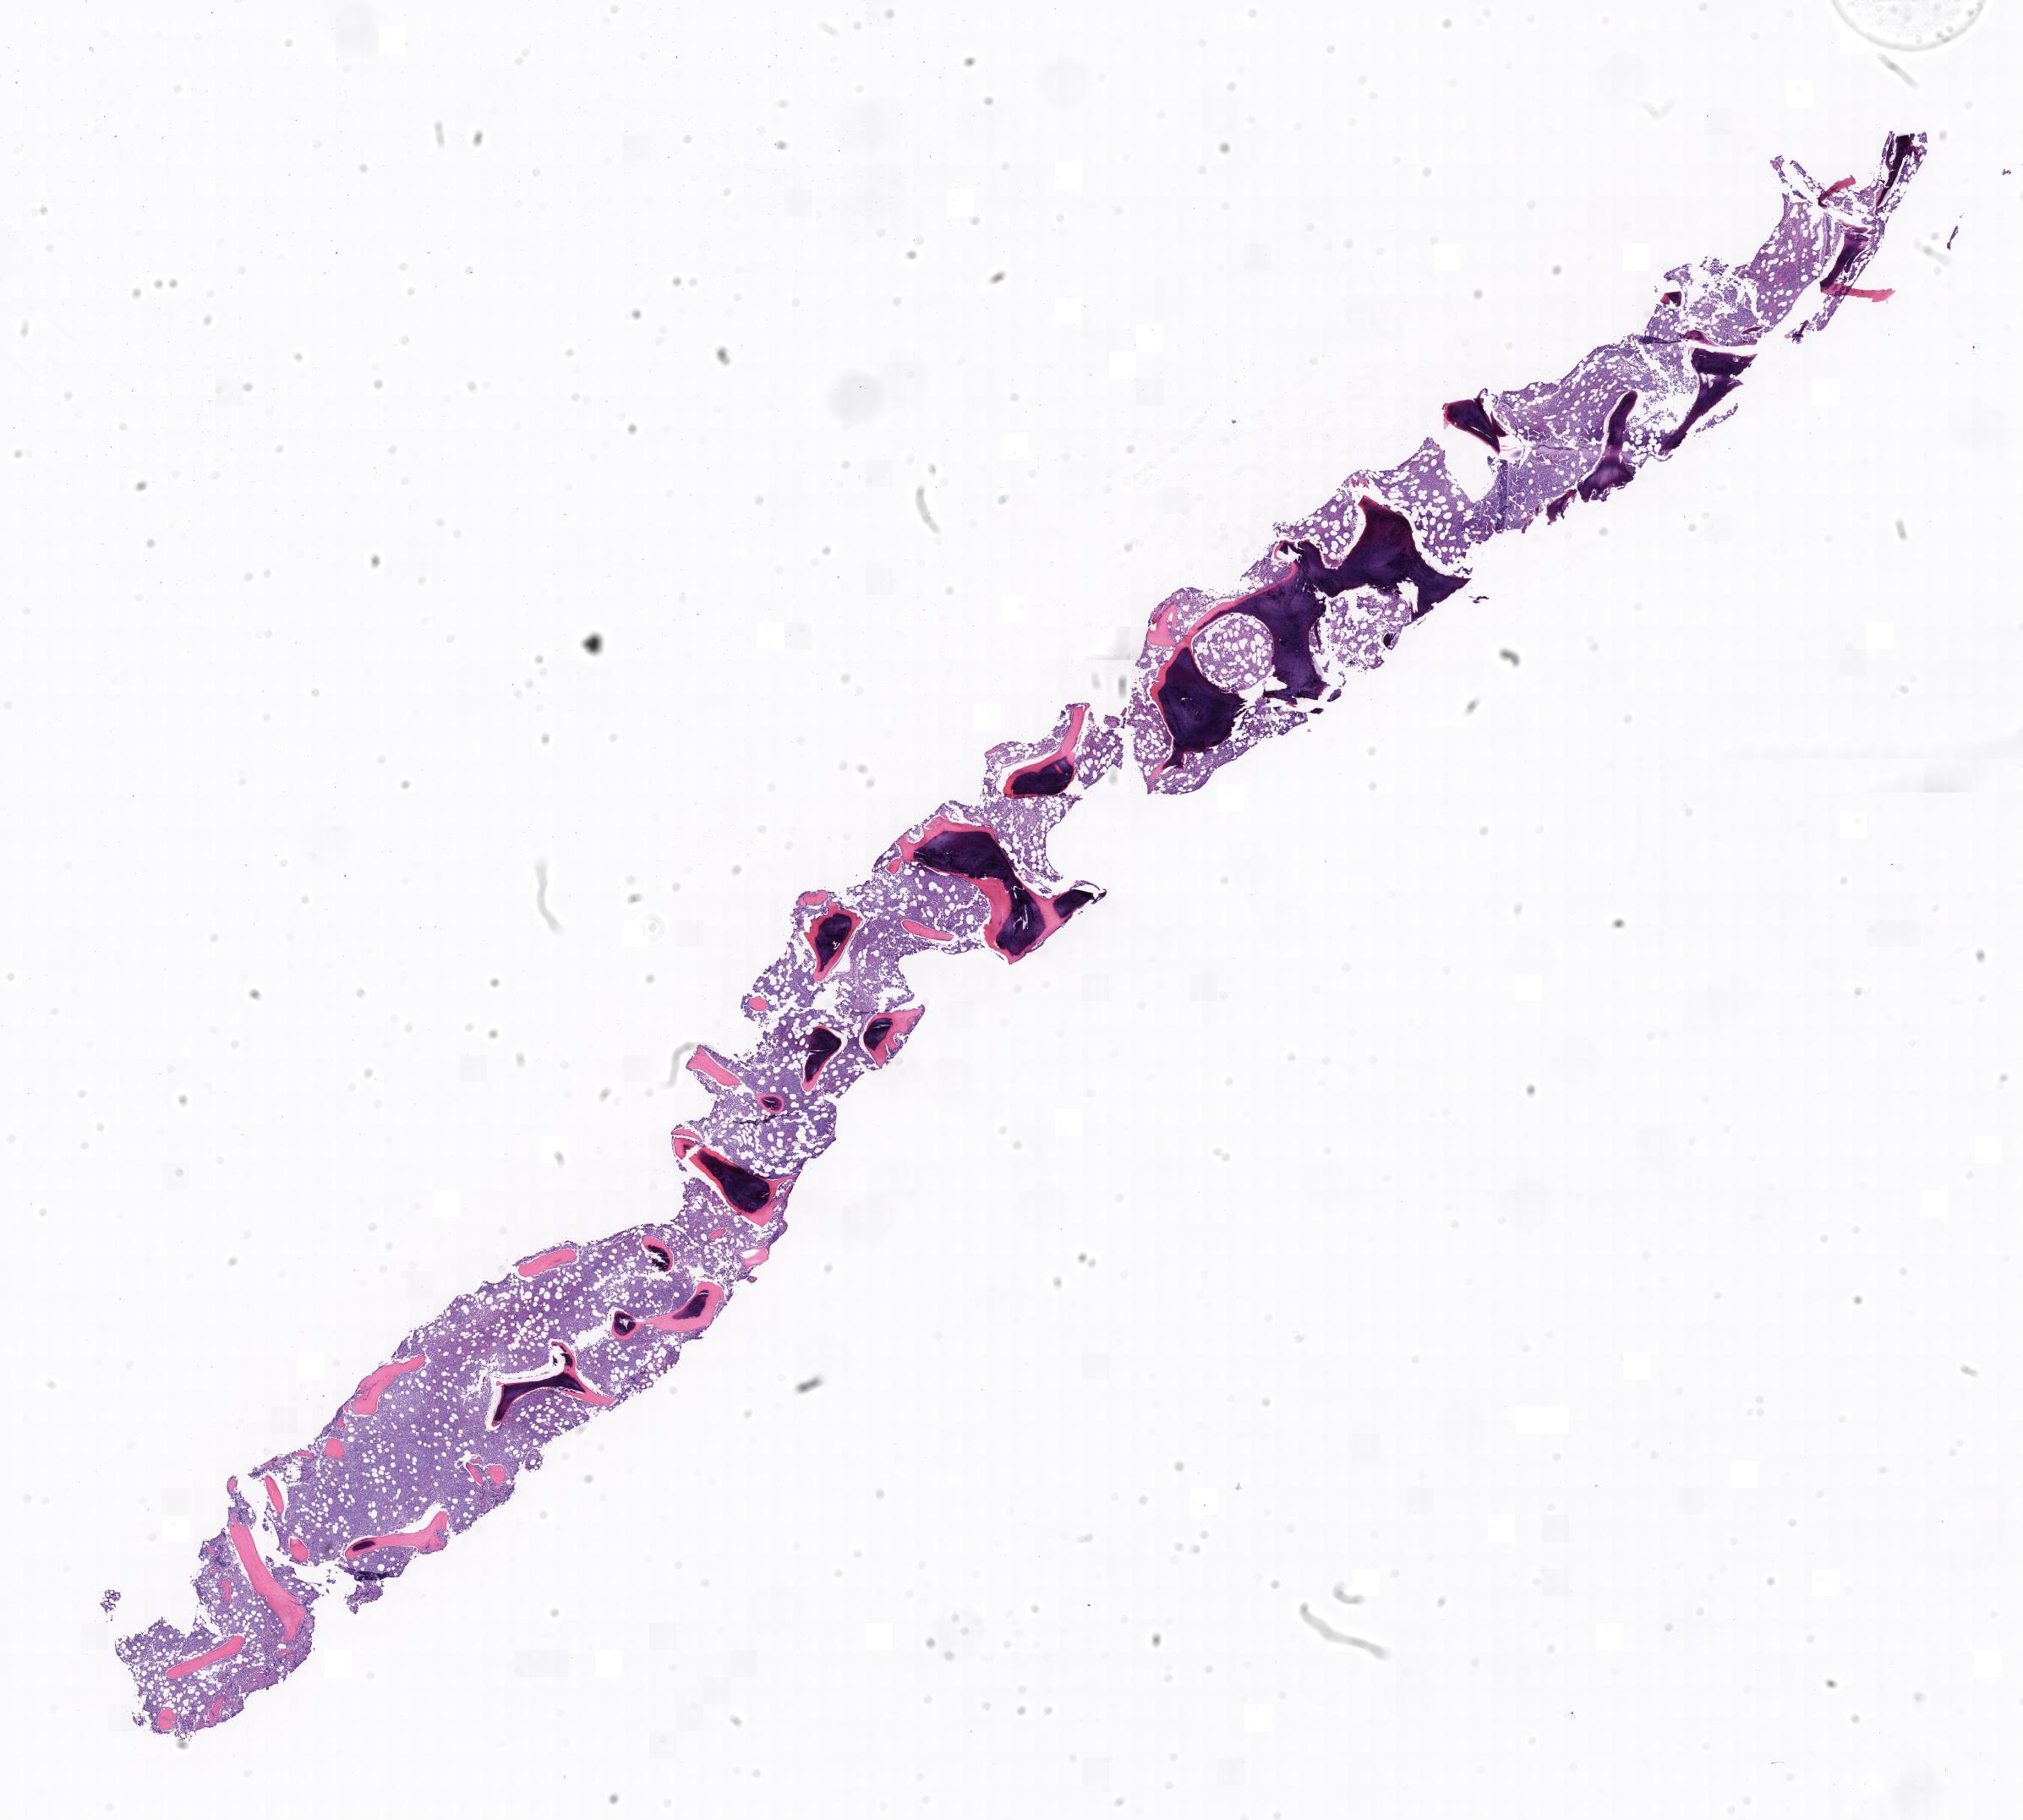
Digitized hematoxylin and eosin (H&E)-stained section, low-resolution overview of the scanned area, specimen: tumor tissue, anatomic site: bone marrow. Patient: male, aged 20.
- histologic diagnosis: Diffuse large B-cell lymphoma, NOS